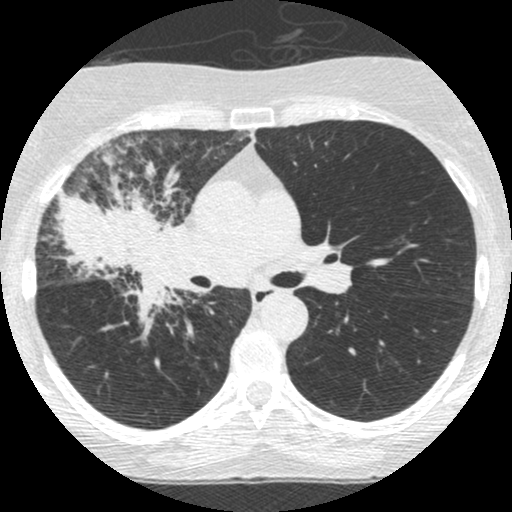
Low-dose screening chest CT, one axial slice. Slice 154 of 253 in the series (ordered by position). Reconstruction kernel STANDARD. 120 kVp. Lung window (W 1500 / L -600 HU). 1.25 mm slice thickness. 512 × 512 image matrix, field of view 294 × 294 mm.
Structures marked on this image (manually delineated by an expert):
- lesion 2 (tumor, hilum of right lung): bounding box (x1, y1, x2, y2) in pixels: (58, 189, 185, 328)